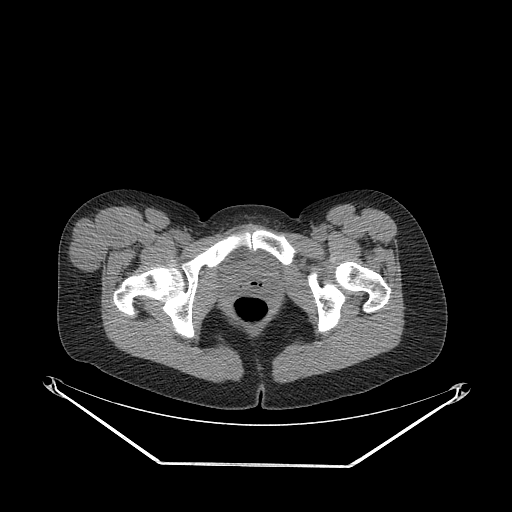
CT of an extremity soft-tissue mass (from a PET/CT study), one axial slice; position 62 of 267 along the scan axis; 140 kVp; soft-tissue window (W 400 / L 40 HU); 512 × 512 image matrix, field of view 500 × 500 mm. Female patient. From the clinical record (not read from this slice): histological type: synovial sarcoma; grade: intermediate; site of the primary tumour: right thigh.
Structures marked on this image (expert contour drawn on MRI and transferred to this co-registered scan by the dataset authors):
- gross tumour volume including surrounding oedema: bounding box [x1, y1, x2, y2] px = [69, 212, 124, 273]
- gross tumour volume (mass): [69, 212, 124, 273]